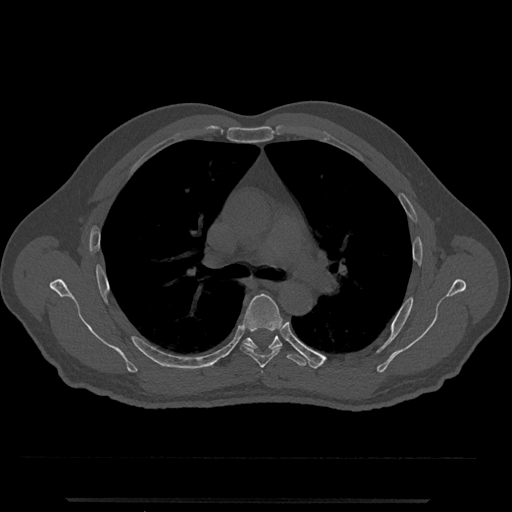
CT including the spine, one axial slice. Position 772 of 797 along the scan axis. Reconstruction kernel Br40s/3. Bone window (W 1800 / L 400 HU). 512 × 512 image matrix, field of view 419 × 419 mm. Patient: male, 63 years. From the clinical record (not read from this slice): primary cancer: prostate.
Outlined on this slice (semi-automatically segmented with operator editing):
- T5 vertebra: bounding box [x1, y1, x2, y2] px = [240, 294, 283, 368]
- T6 vertebra: [243, 335, 307, 367]